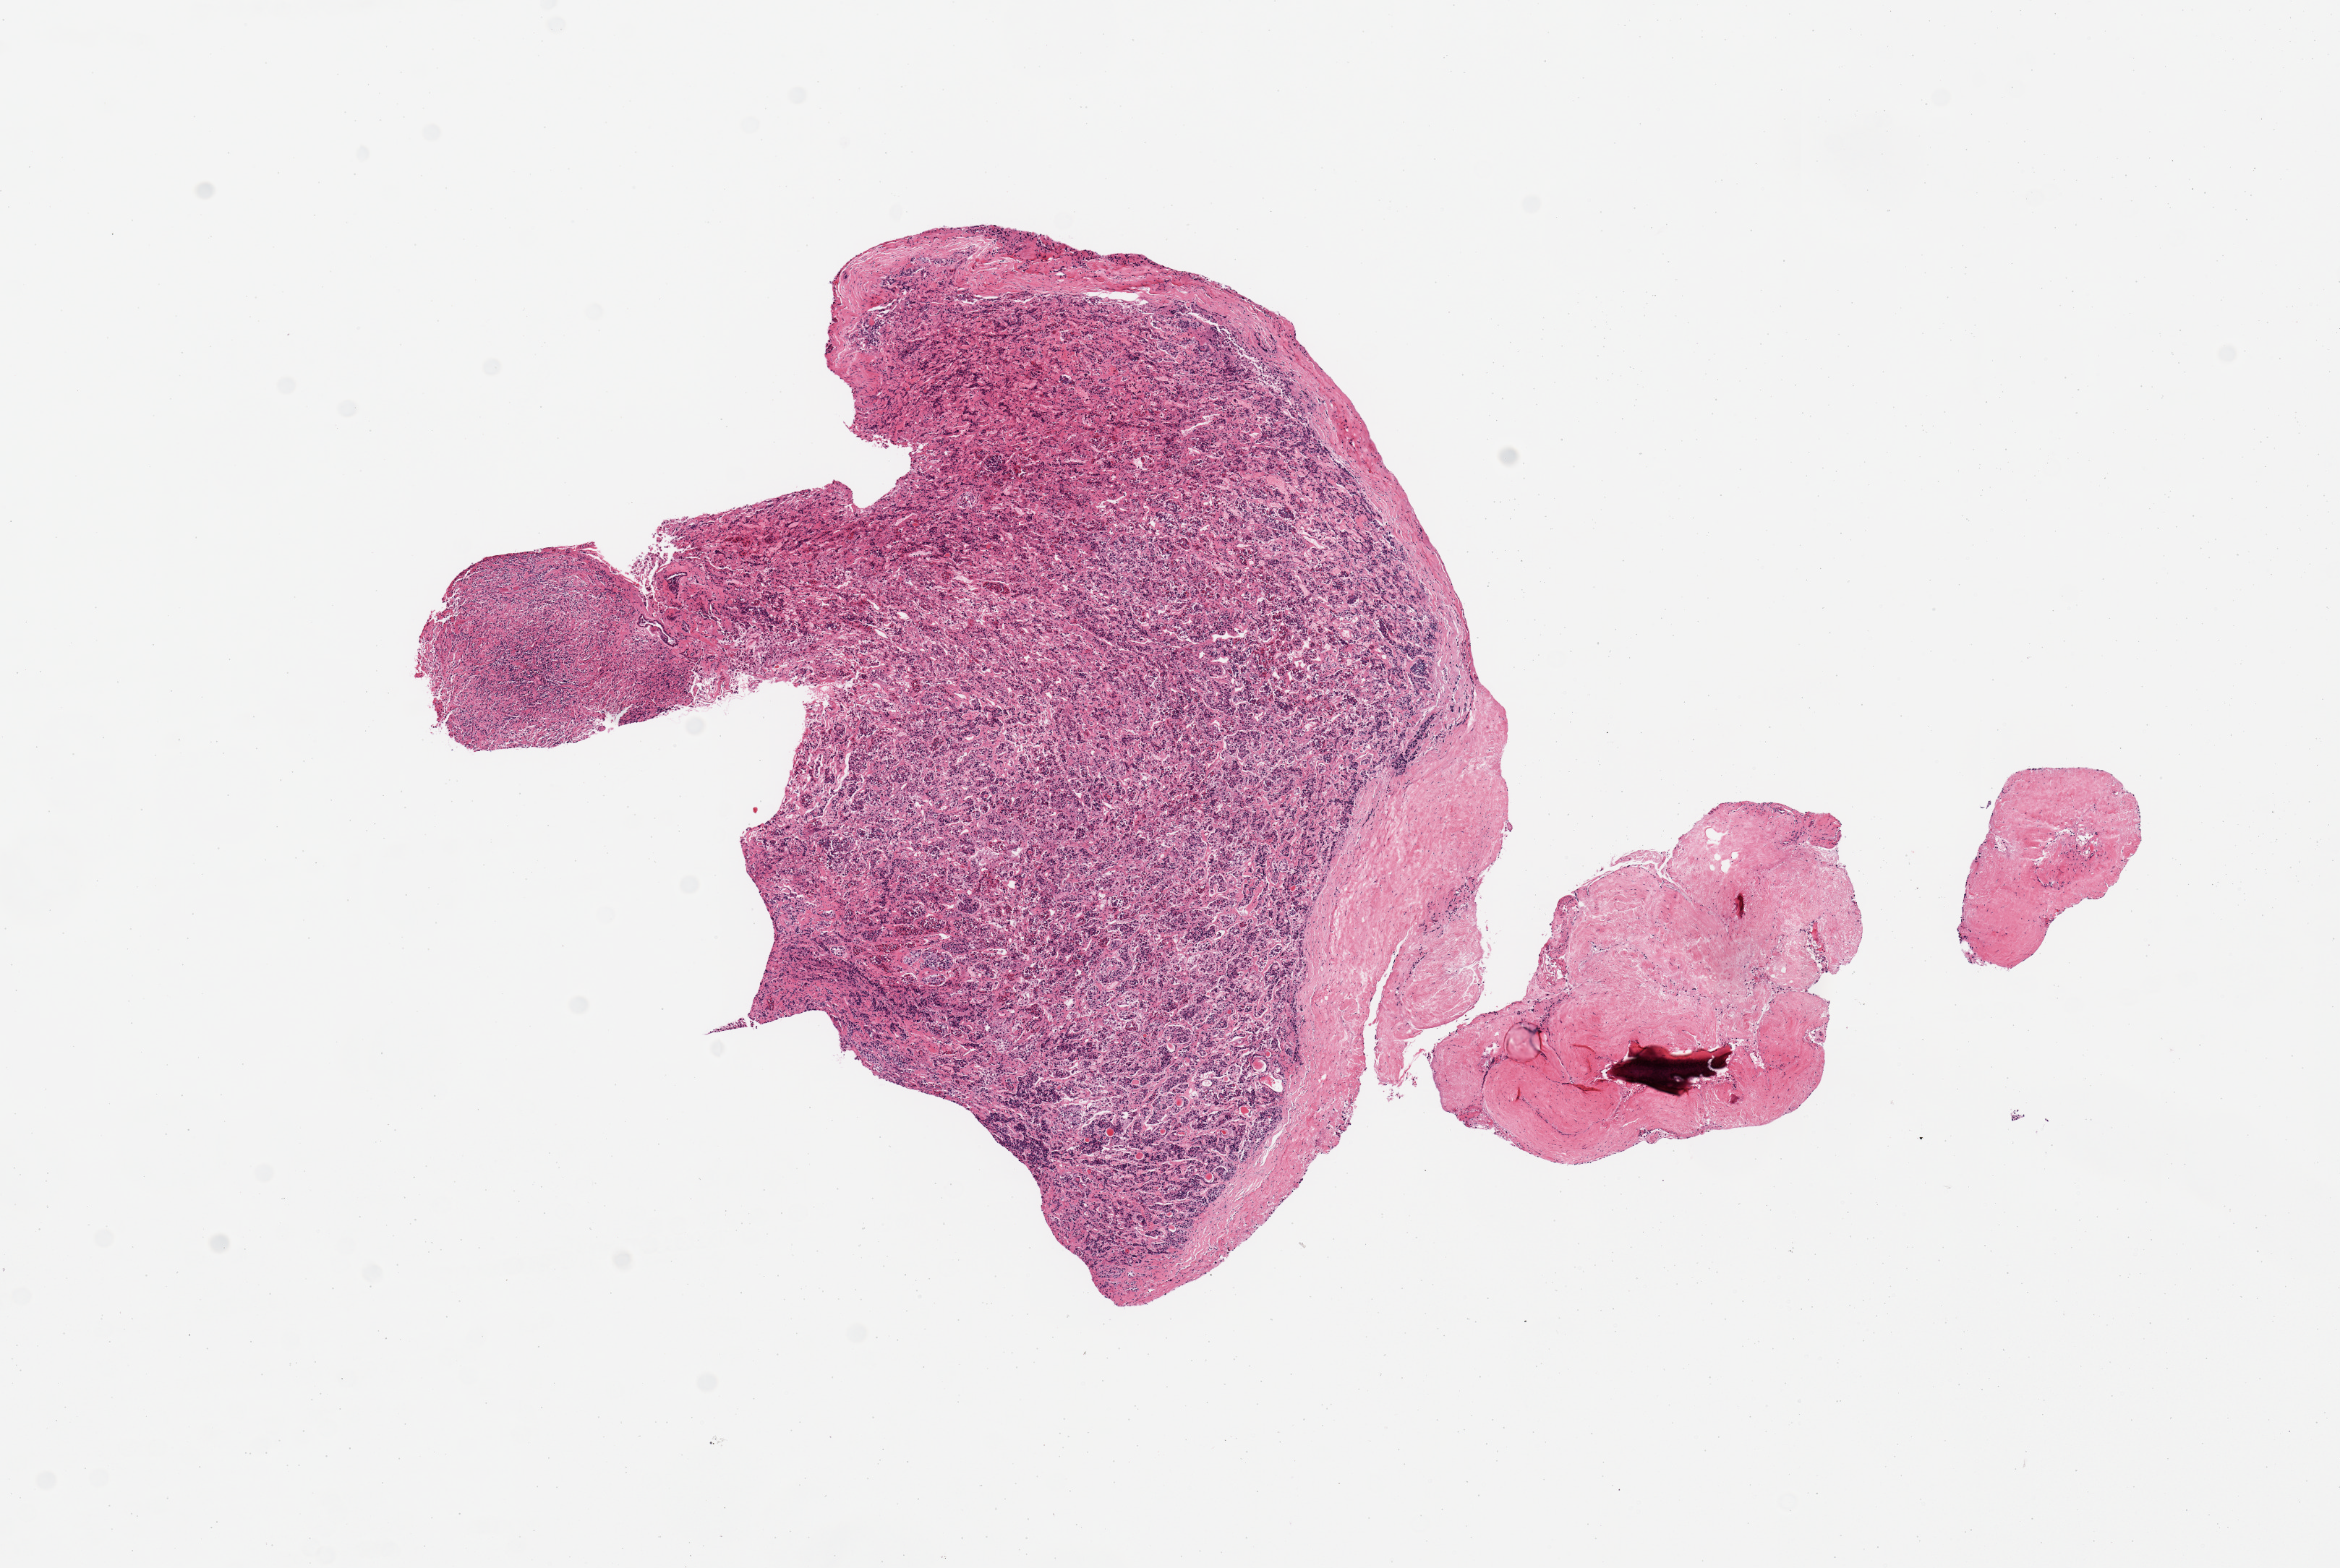
Digitized H&E-stained section, low-resolution overview of the scanned area, about 12.8 x 8.6 mm; PAXgene-fixed, paraffin-embedded tissue; section of pituitary (target tissue); tissue donor sample.
Review note (as recorded): 1 piece, adenohypophysis, neurohypophysis, and small portion of pars intermedia.